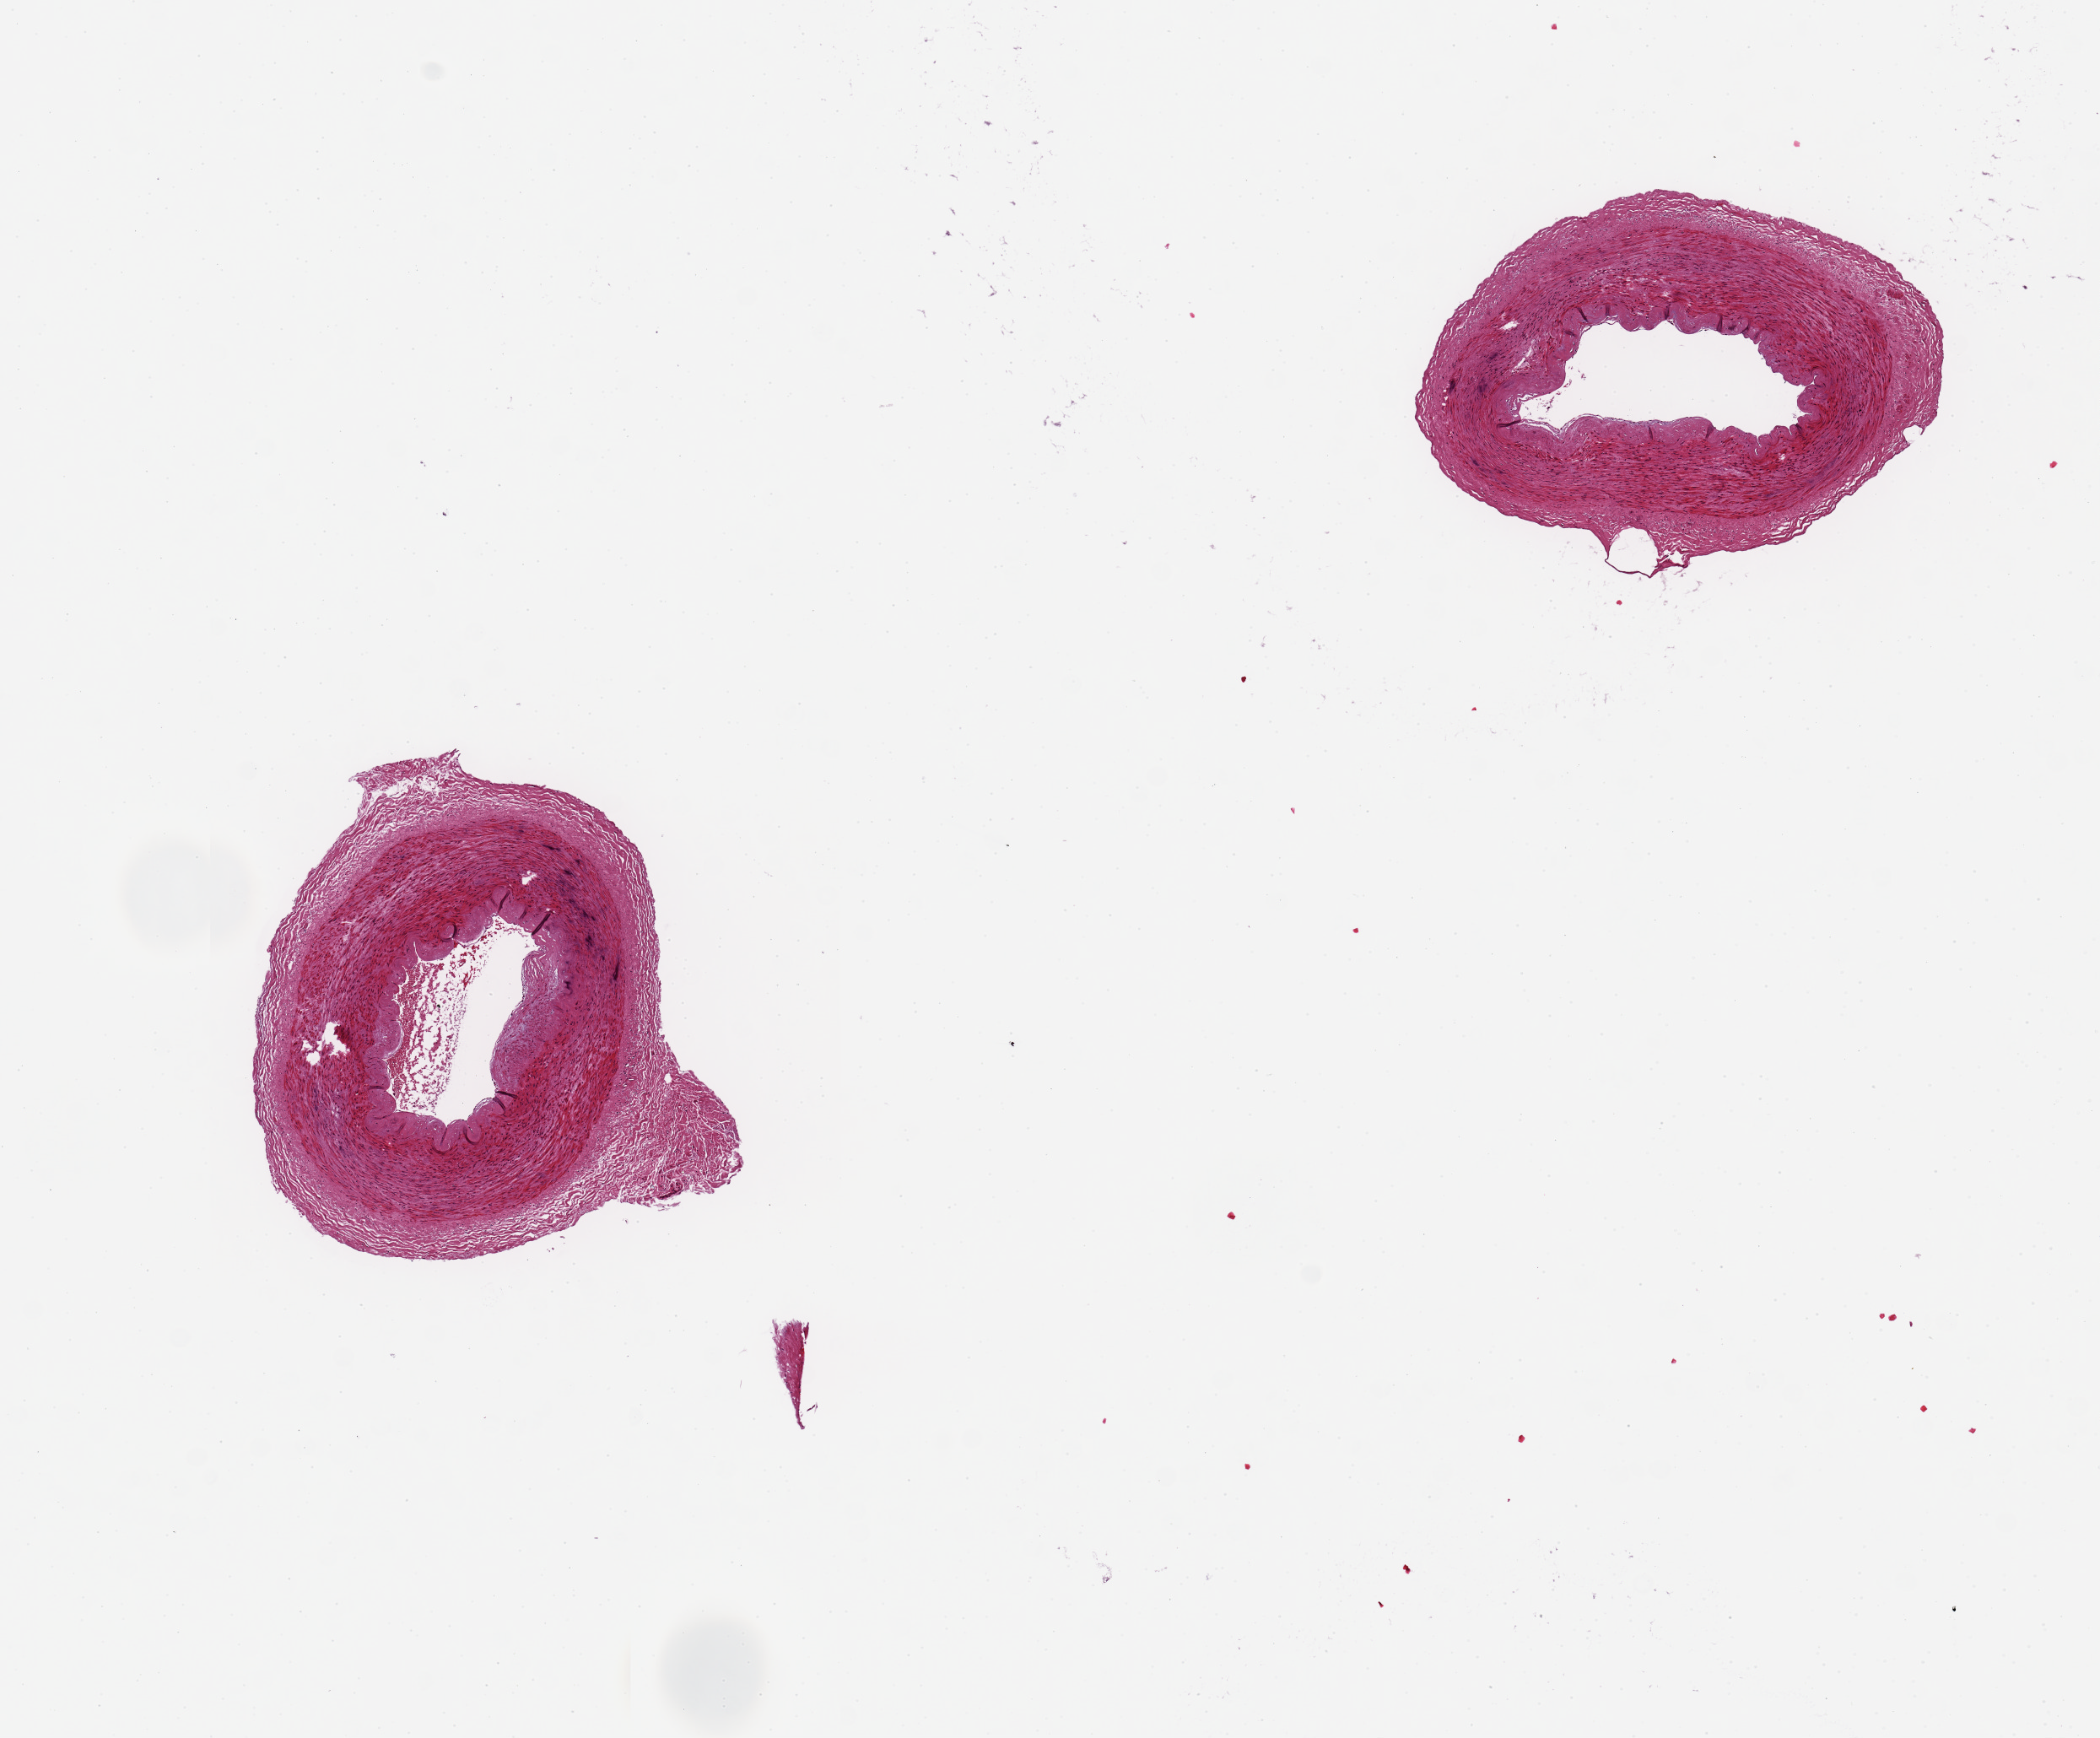
Digitized H&E-stained section, shown as a low-resolution overview of the whole scanned area (about 9.8 x 8.1 mm, slide scanned at 20x), PAXgene-fixed, paraffin-embedded tissue, sampled site (target tissue): tibial artery, donor tissue sample.
Review note (as recorded): 2 pieces ~2 mm diameter; no lesions; cleaned of adipose.